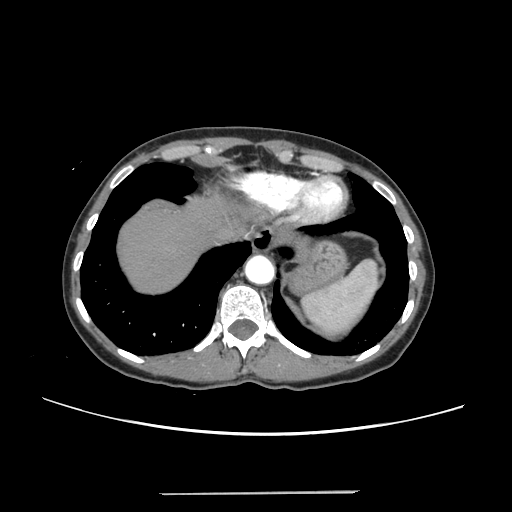
Contrast-enhanced abdominal CT, one axial slice; slice 216 of 240 in the series (ordered by position); 120 kVp; intravenous contrast given; soft-tissue window (W 400 / L 40 HU); 1.25 mm slice thickness; 512 × 512 image matrix, field of view 371 × 371 mm. Female patient, age 60 years. Case-level facts recorded for this patient, not image findings: diagnosis: colorectal cancer liver metastases, imaged before liver resection; multiple liver metastases: no; largest metastasis: 1.5 cm; disease in both lobes: no.
Structures marked on this image (expert manual segmentation):
- liver: bounding box <119,198,235,292> (left, top, right, bottom; pixels)
- planned liver remnant (the part of the liver to remain after resection): <119,198,235,292>